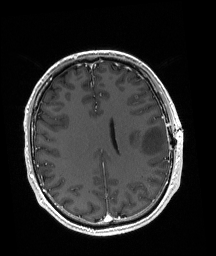
Brain MRI from a brain-tumour surgery series, one axial slice. Slice 73 of 192 in the series (ordered by position). T1-weighted post-contrast. 216 × 256 image matrix, field of view 211 × 250 mm. From the clinical record (not read from this slice): histopathology: Astrocytoma; WHO grade: 3; IDH mutation: yes; tumour location: Left Posterior Frontal.
Structures marked on this image (expert manual segmentation):
- tumour: bounding box <130,126,166,155> (left, top, right, bottom; pixels)